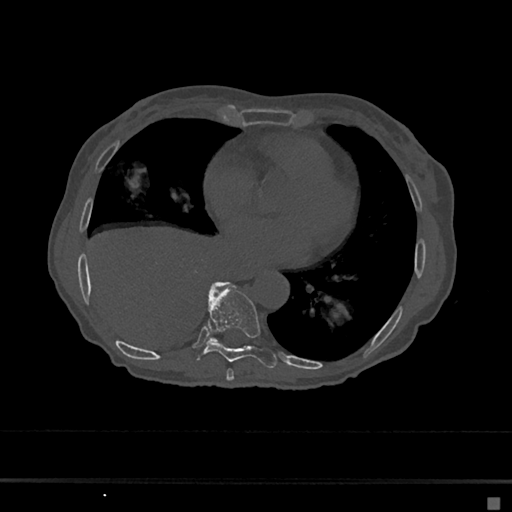
CT including the spine, one axial slice; slice 319 of 797 in the series (ordered by position); reconstruction kernel Br40s/3; bone window (W 1800 / L 400 HU); 0.5 mm slice thickness; 512 × 512 image matrix. Patient: female, 68 years. Case-level facts recorded for this patient, not image findings: primary cancer: renal.
Outlined on this slice (semi-automatic segmentation, software-assisted and operator-edited):
- T7 vertebra: box from (x=226, y=369) to (x=234, y=381) px
- T8 vertebra: (x=196, y=282)–(x=277, y=369)
- T9 vertebra: (x=211, y=281)–(x=224, y=342)